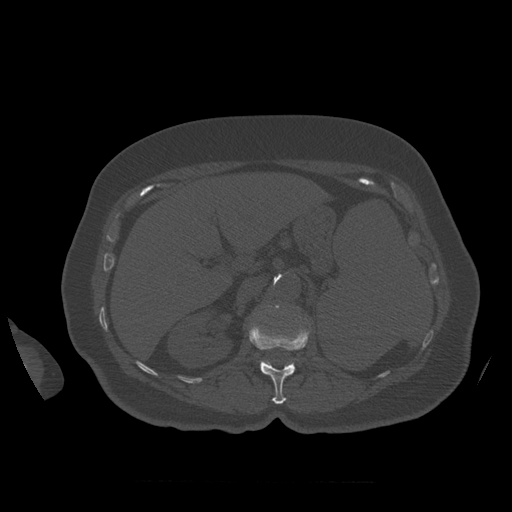
CT including the spine, one axial slice. Position 272 of 399 along the scan axis. 120 kVp. Bone window (W 1800 / L 400 HU). 1.25 mm slice thickness. 512 × 512 image matrix, field of view 404 × 404 mm. Patient age 81 years. Case-level facts recorded for this patient, not image findings: primary cancer: renal; vertebrae with lytic lesions (as recorded): L1.
Outlined on this slice (semi-automatic segmentation, software-assisted and operator-edited):
- L1 vertebra: bounding box [x1, y1, x2, y2] px = [249, 324, 309, 404]
- L2 vertebra: [269, 305, 280, 312]